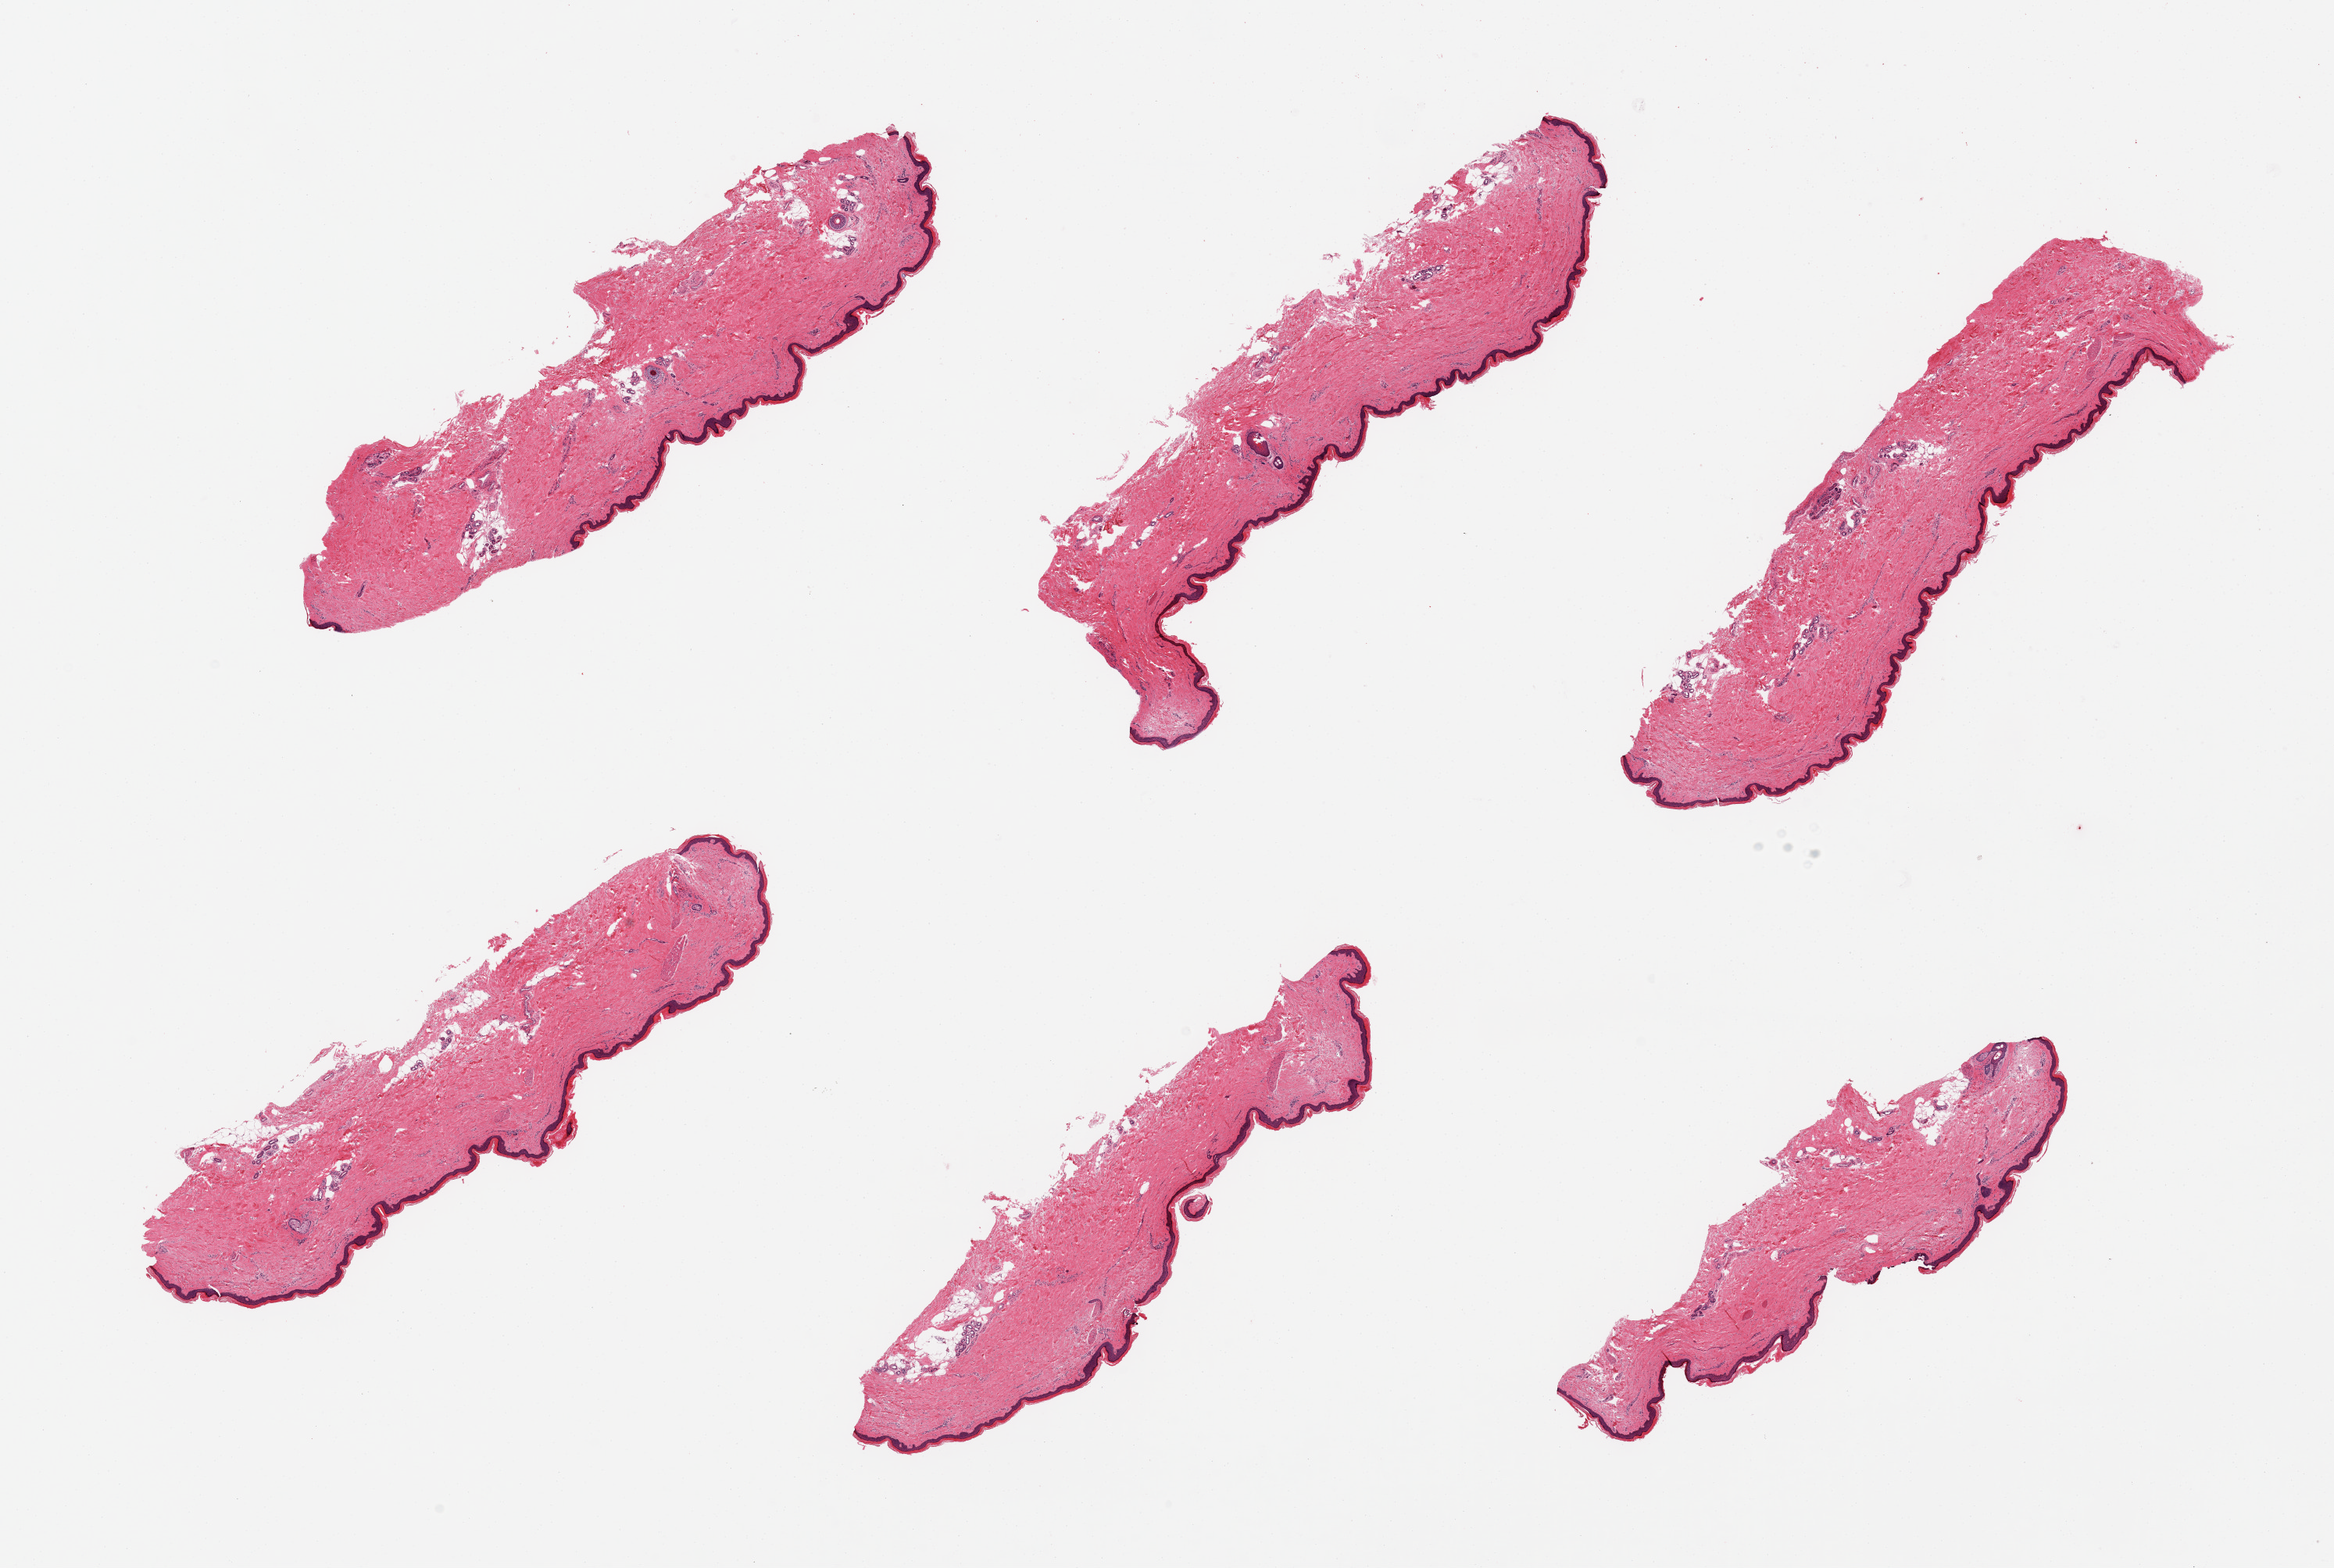
Whole-slide image, haematoxylin and eosin stain, whole scanned area (about 23.6 x 15.9 mm, slide scanned at 20x) shown as a low-resolution overview. PAXgene-fixed, paraffin-embedded tissue. Target tissue: skin of lower leg. Donor tissue sample. Female donor.
* pathologist's review note for this sample: 6 pieces; well trimmed; 5-10% dermal fat